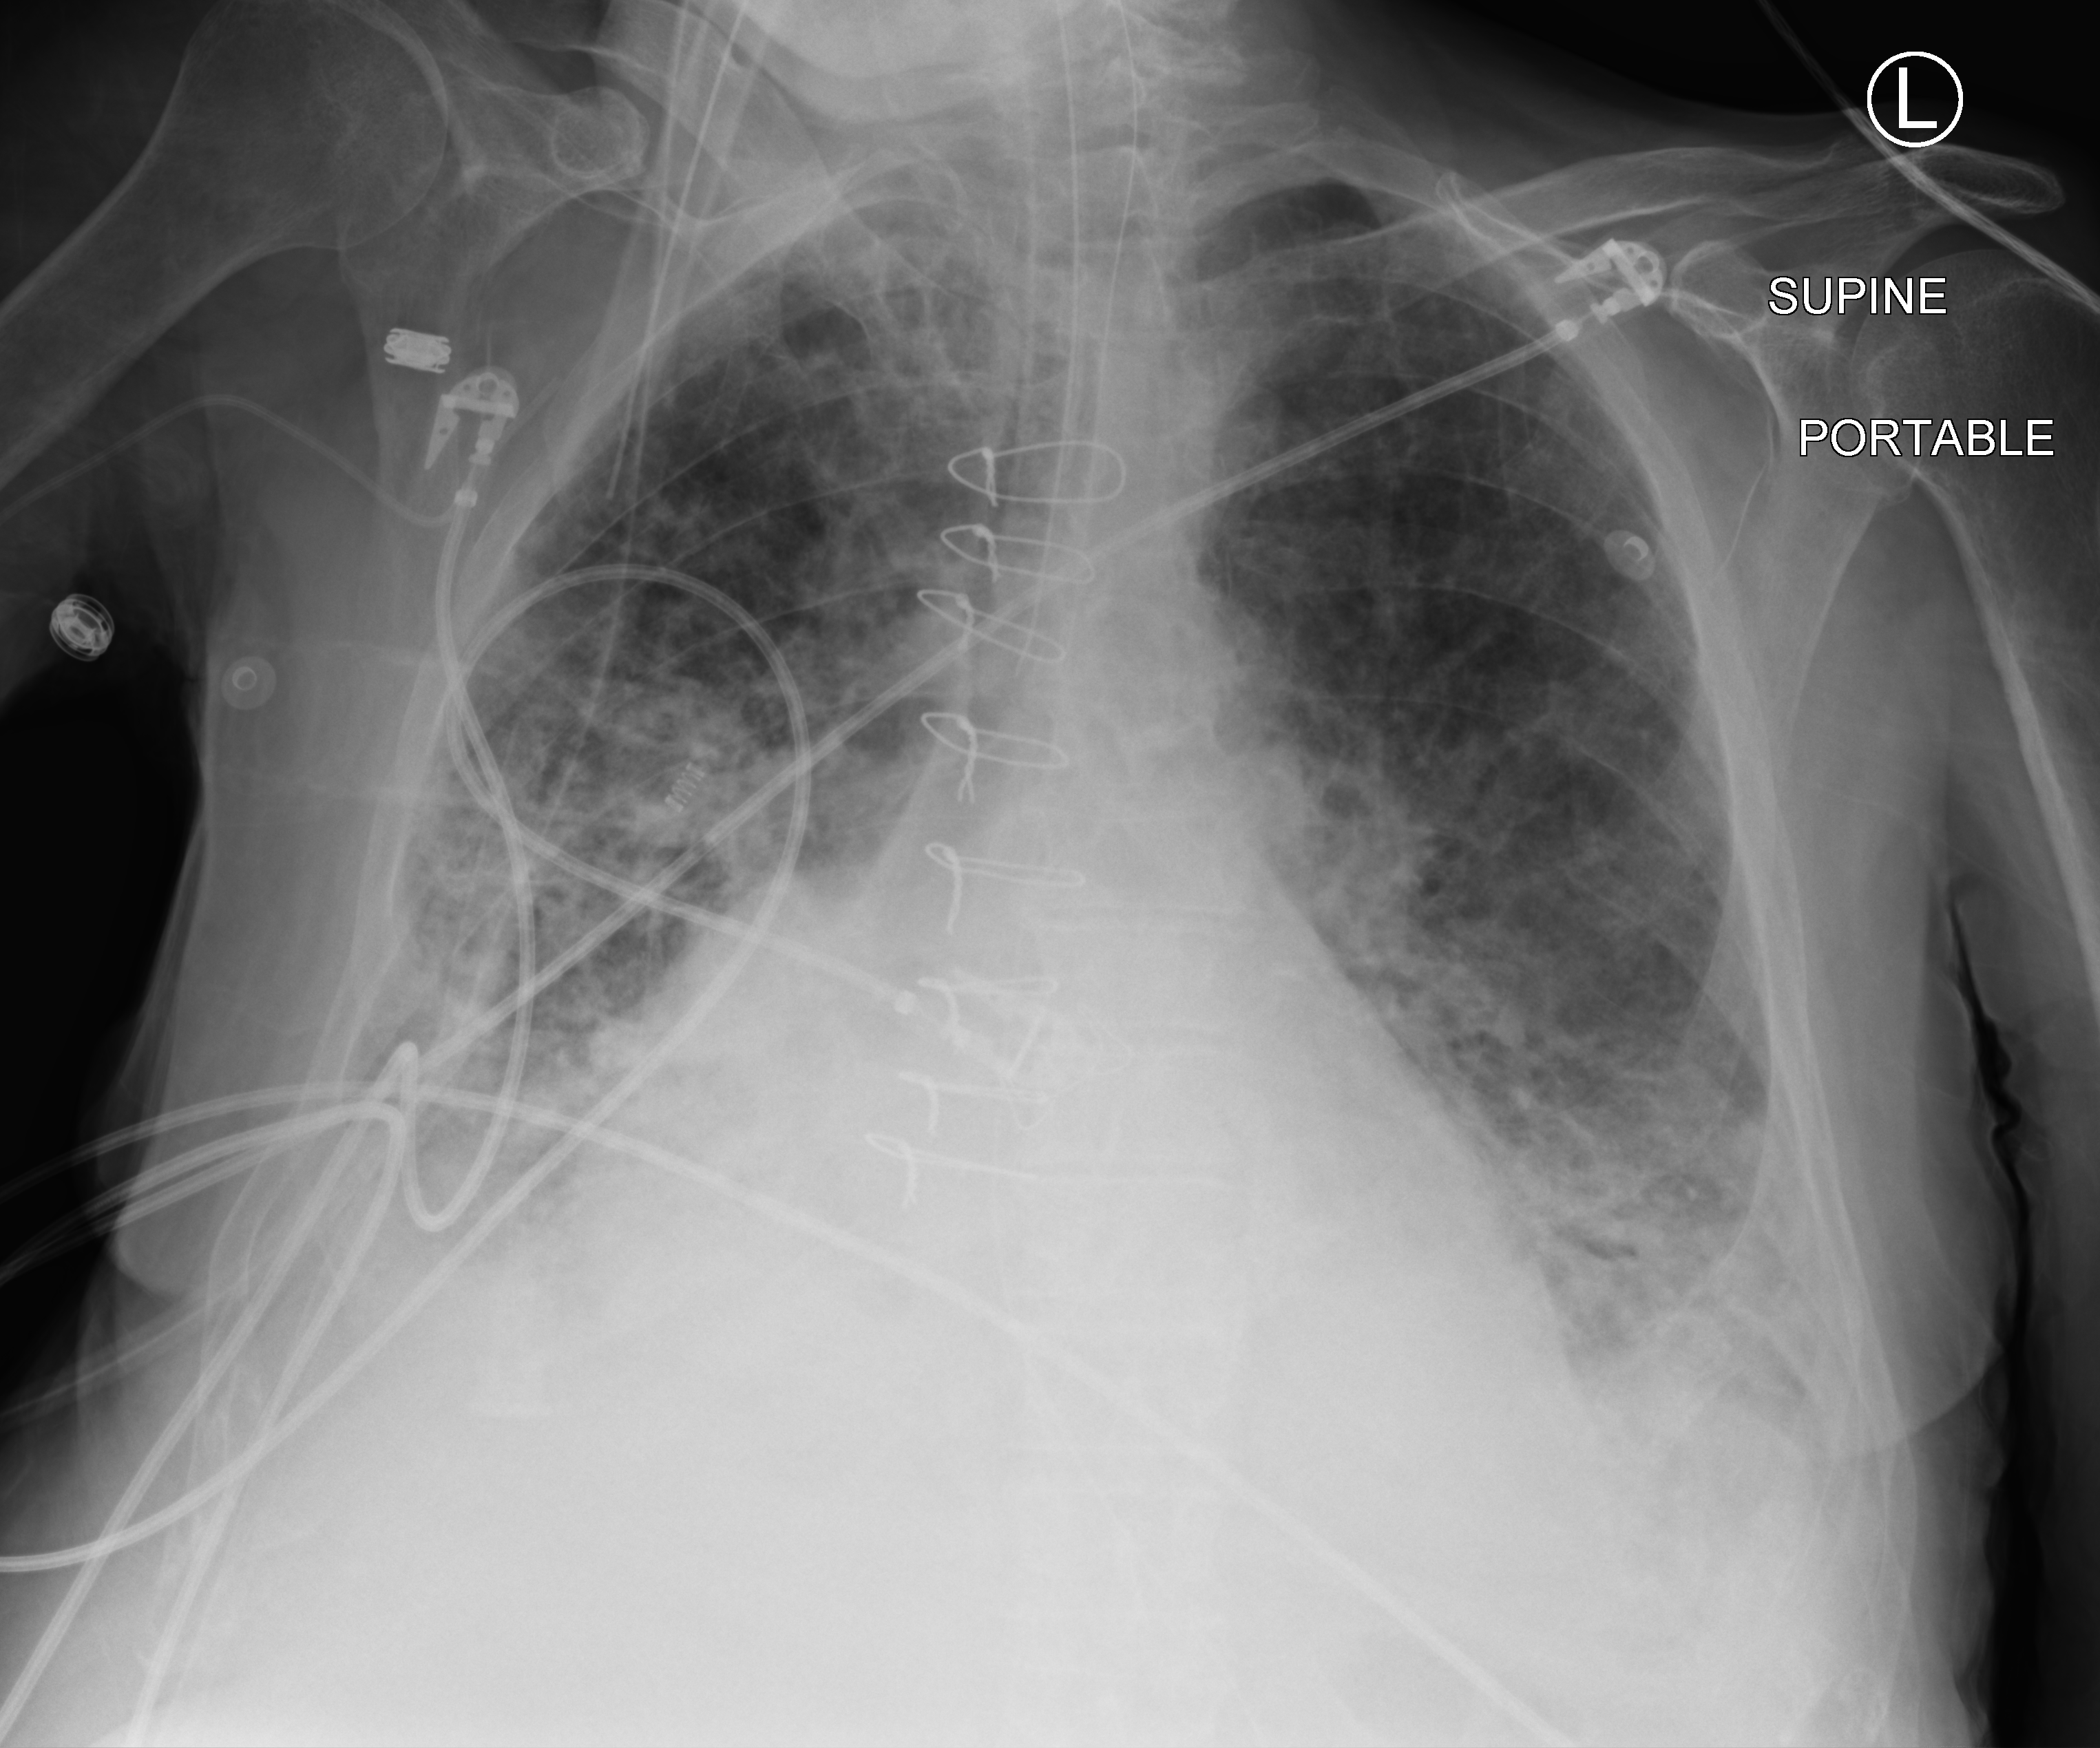
Portable chest radiograph. Patient hospitalised with COVID-19; male, aged 75–90 years.
Admission-level facts for this patient (not findings on this image; timing relative to this image not recorded): mechanically ventilated during this hospital stay: yes; admitted to intensive care during this hospital stay: yes; length of hospital stay: 40 days.